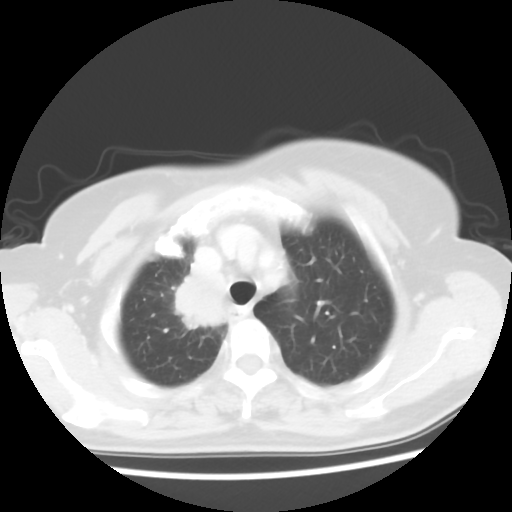
Chest CT, one axial slice; position 46 of 56 along the scan axis; reconstruction kernel STANDARD; lung window (W 1500 / L -600 HU); 5 mm slice thickness; 512 × 512 image matrix. Patient: female, 62 years. Case-level facts recorded for this patient, not image findings: clinical TNM (as recorded): T2 N1 M1a.
Annotated regions visible in this slice (bounding box drawn by a radiologist):
- lung tumour (recorded histology: adenocarcinoma): box from (x=171, y=267) to (x=237, y=338) px